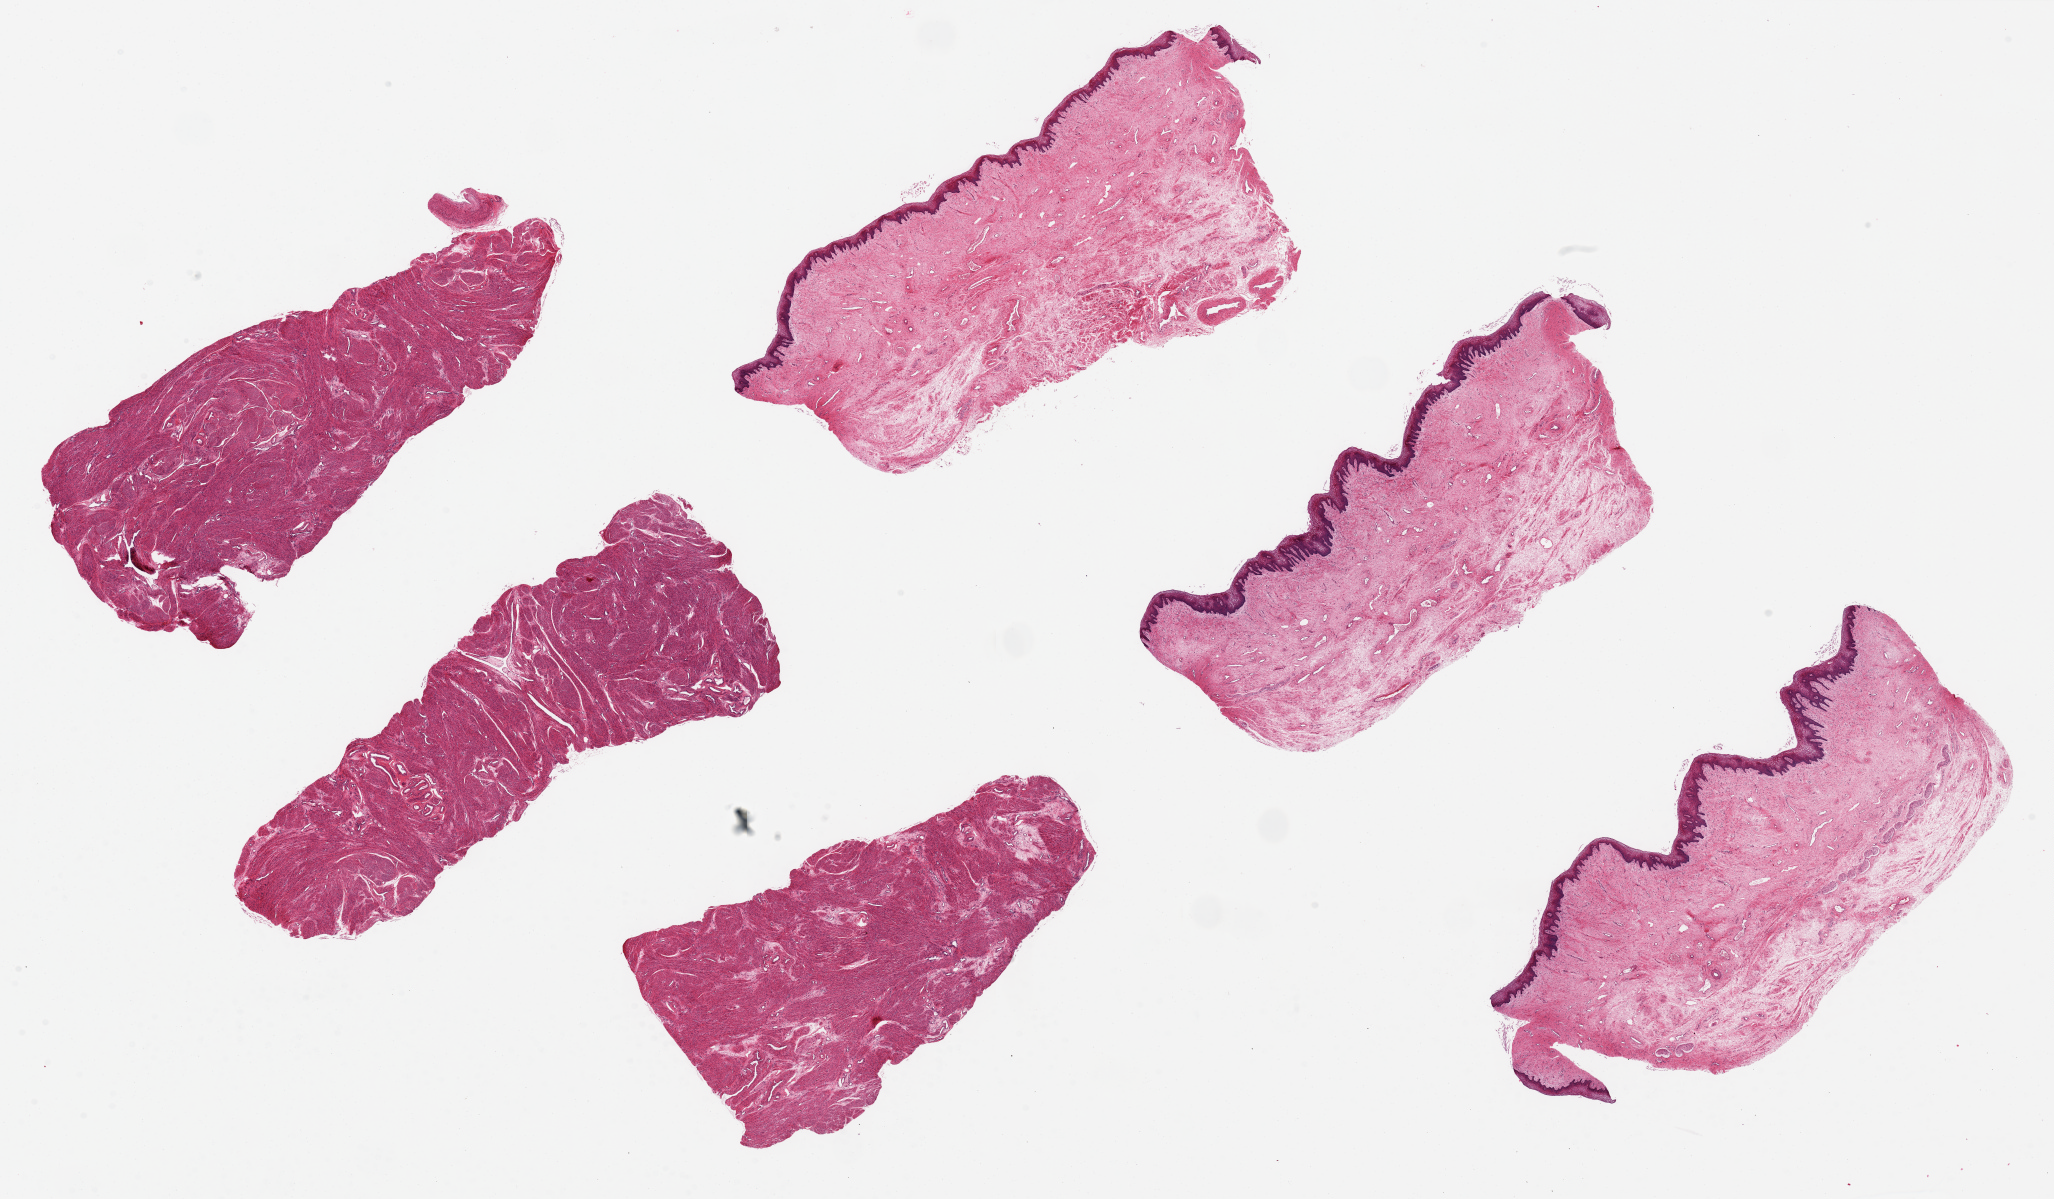
Digitized haematoxylin and eosin-stained section — shown as a low-resolution overview of the whole scanned area (about 32.5 x 19.0 mm), PAXgene-fixed paraffin-embedded (PFPE) section, sampled site (target tissue): vagina, tissue donor sample. Donor: female.
Pathologist's review note for this sample: 6 pieces, ~8x3mm Only 3 show squamous mucosa and submucosa; 3 are smooth muscle, unknown provenance.